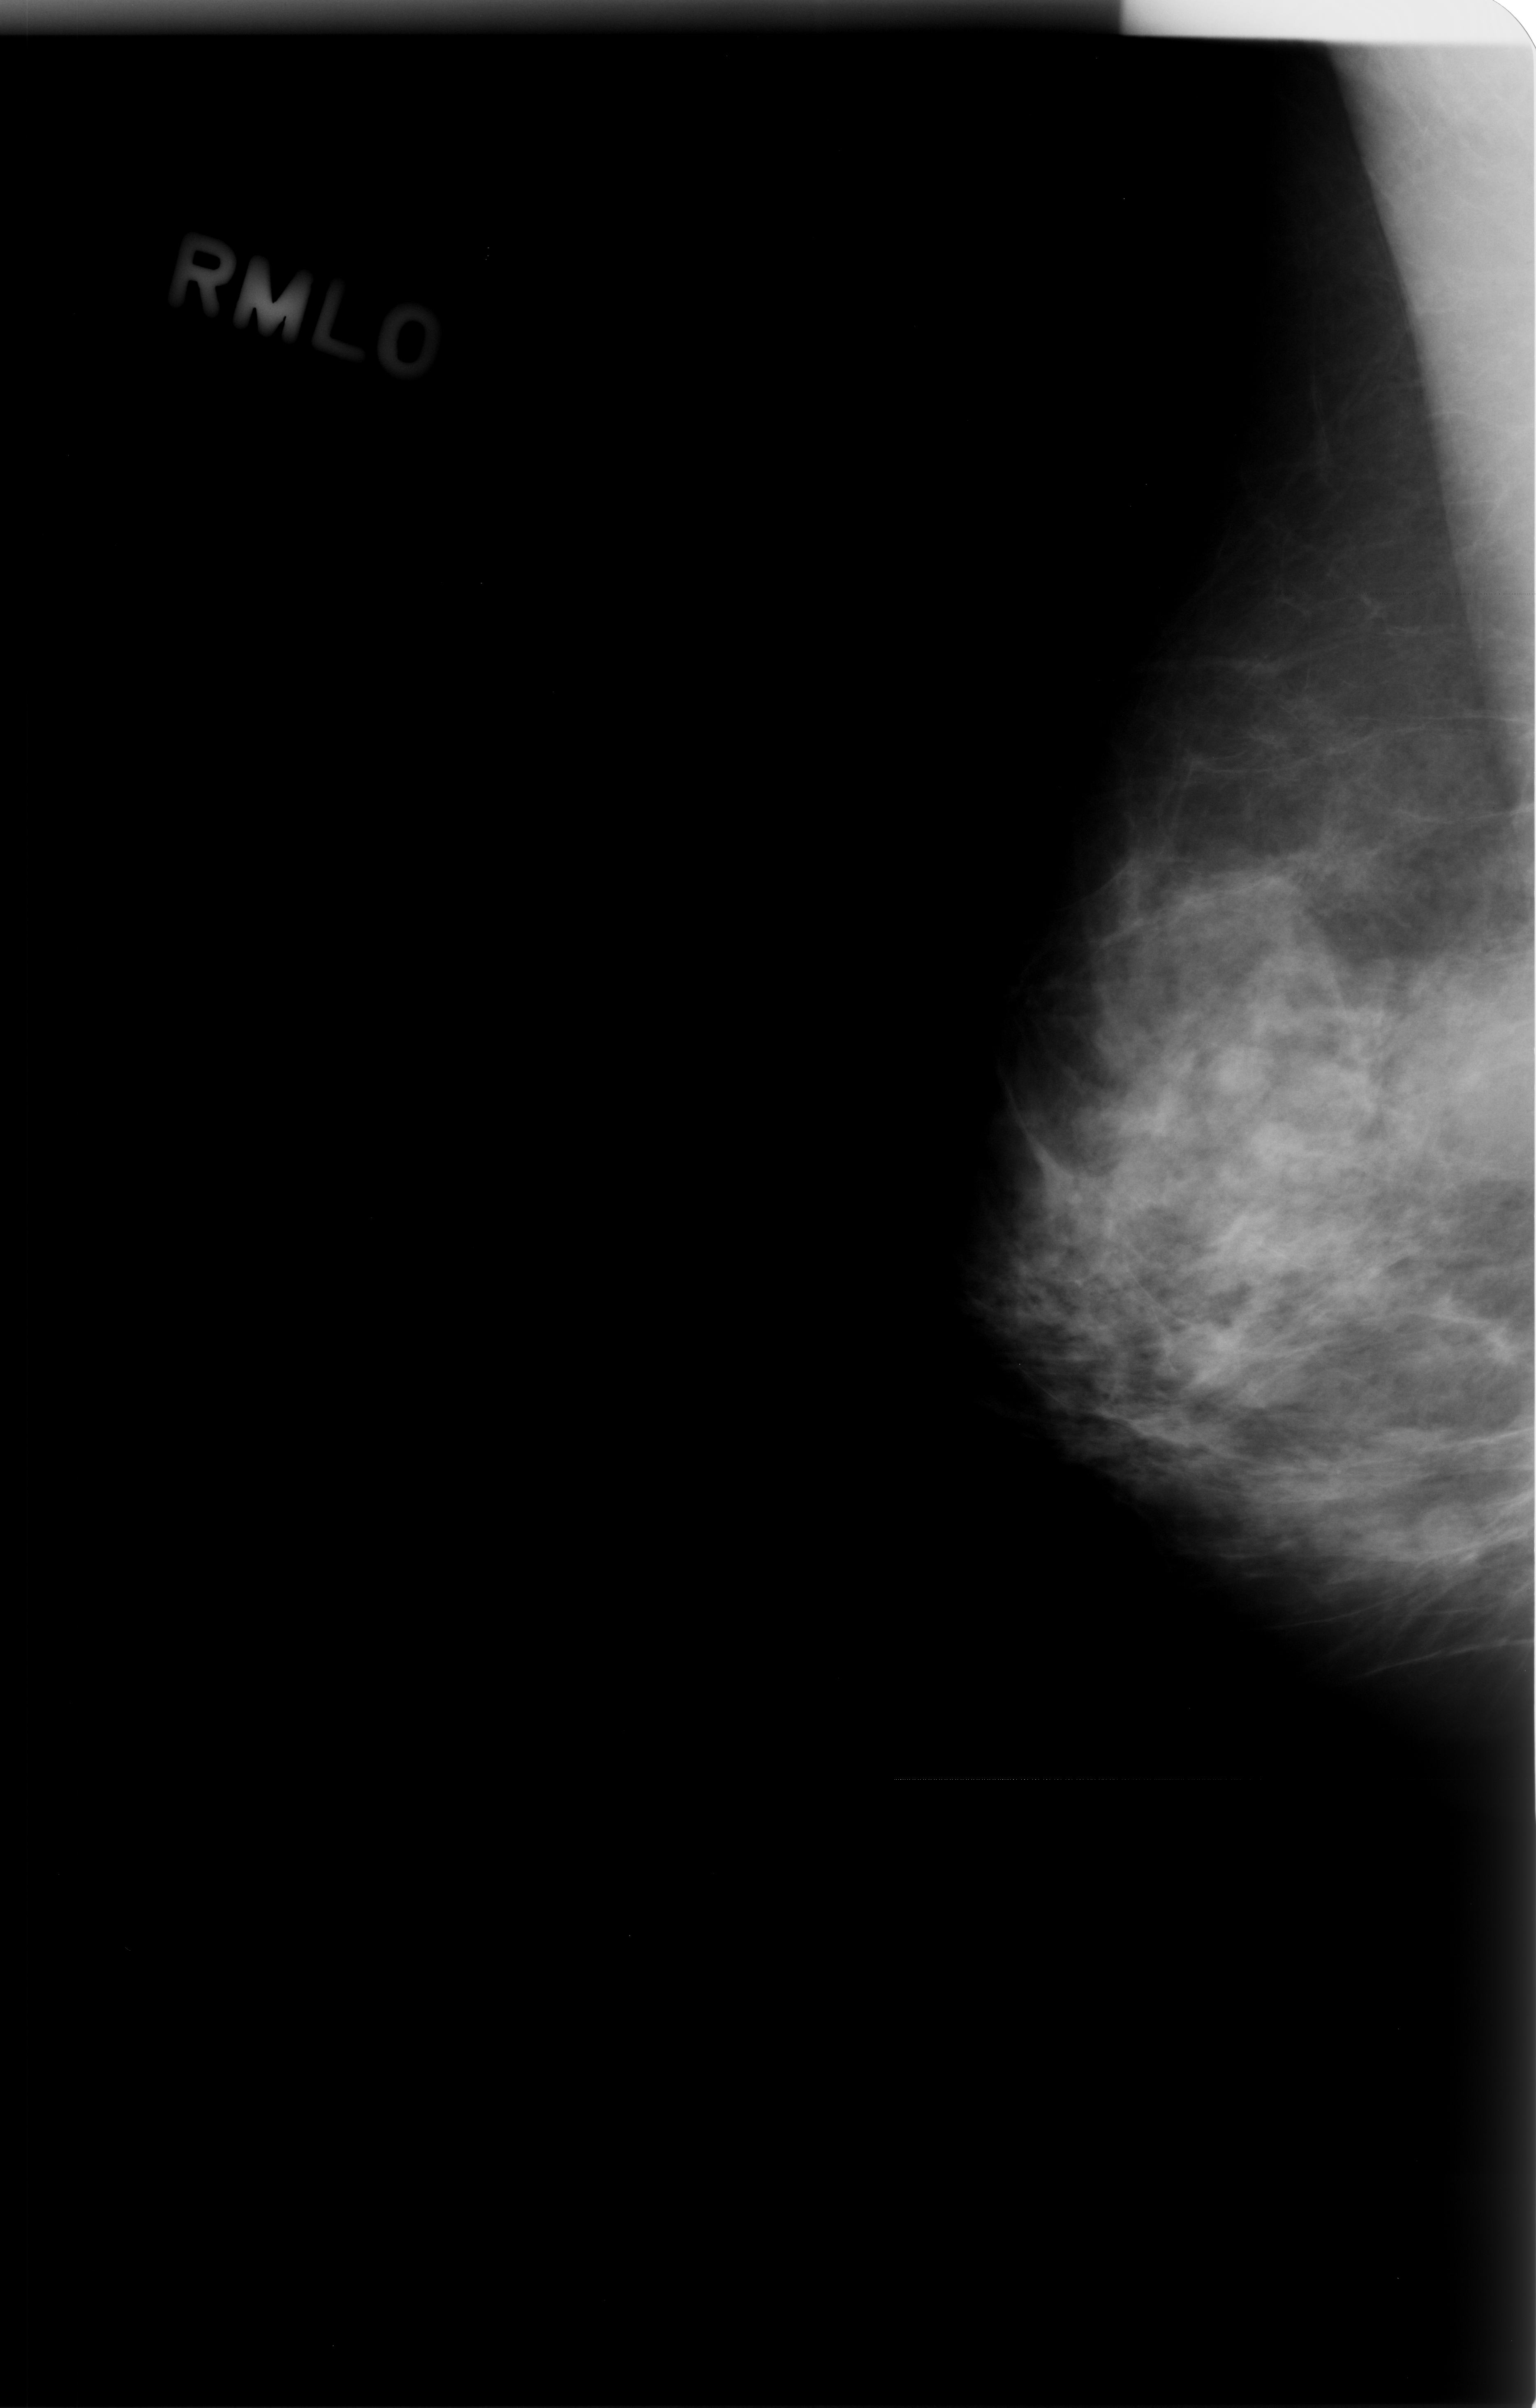
Digitized screen-film mammogram. Right breast. Mediolateral oblique (MLO) view. Breast composition: heterogeneously dense (BI-RADS density category 3 of 4). 1536 × 2408 image matrix.
Marked abnormalities (boxes around the expert regions of interest):
- mass, shape oval, margins obscured; BI-RADS assessment category 3; subtlety rating 4 on a 1 (subtle) to 5 (obvious) scale; pathology result (as recorded, not read from the image): benign: bounding box (x1, y1, x2, y2) in pixels: (1399, 946, 1536, 1198)